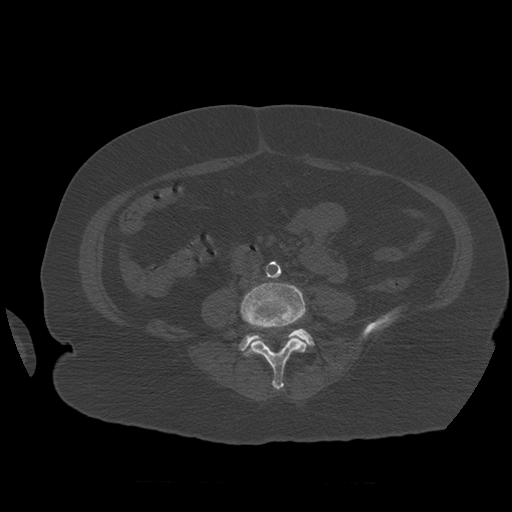
CT including the spine, one axial slice. Position 198 of 399 along the scan axis. Reconstruction kernel STANDARD. 120 kVp. Bone window (W 1800 / L 400 HU). 1.25 mm slice thickness. 512 × 512 image matrix, field of view 404 × 404 mm. Patient age 81 years. From the clinical record (not read from this slice): primary cancer: renal; vertebrae with lytic lesions (as recorded): L1.
Outlined on this slice (semi-automatically segmented with operator editing):
- L4 vertebra: bounding box (x1, y1, x2, y2) in pixels: (241, 283, 308, 390)
- L5 vertebra: (240, 329, 315, 353)